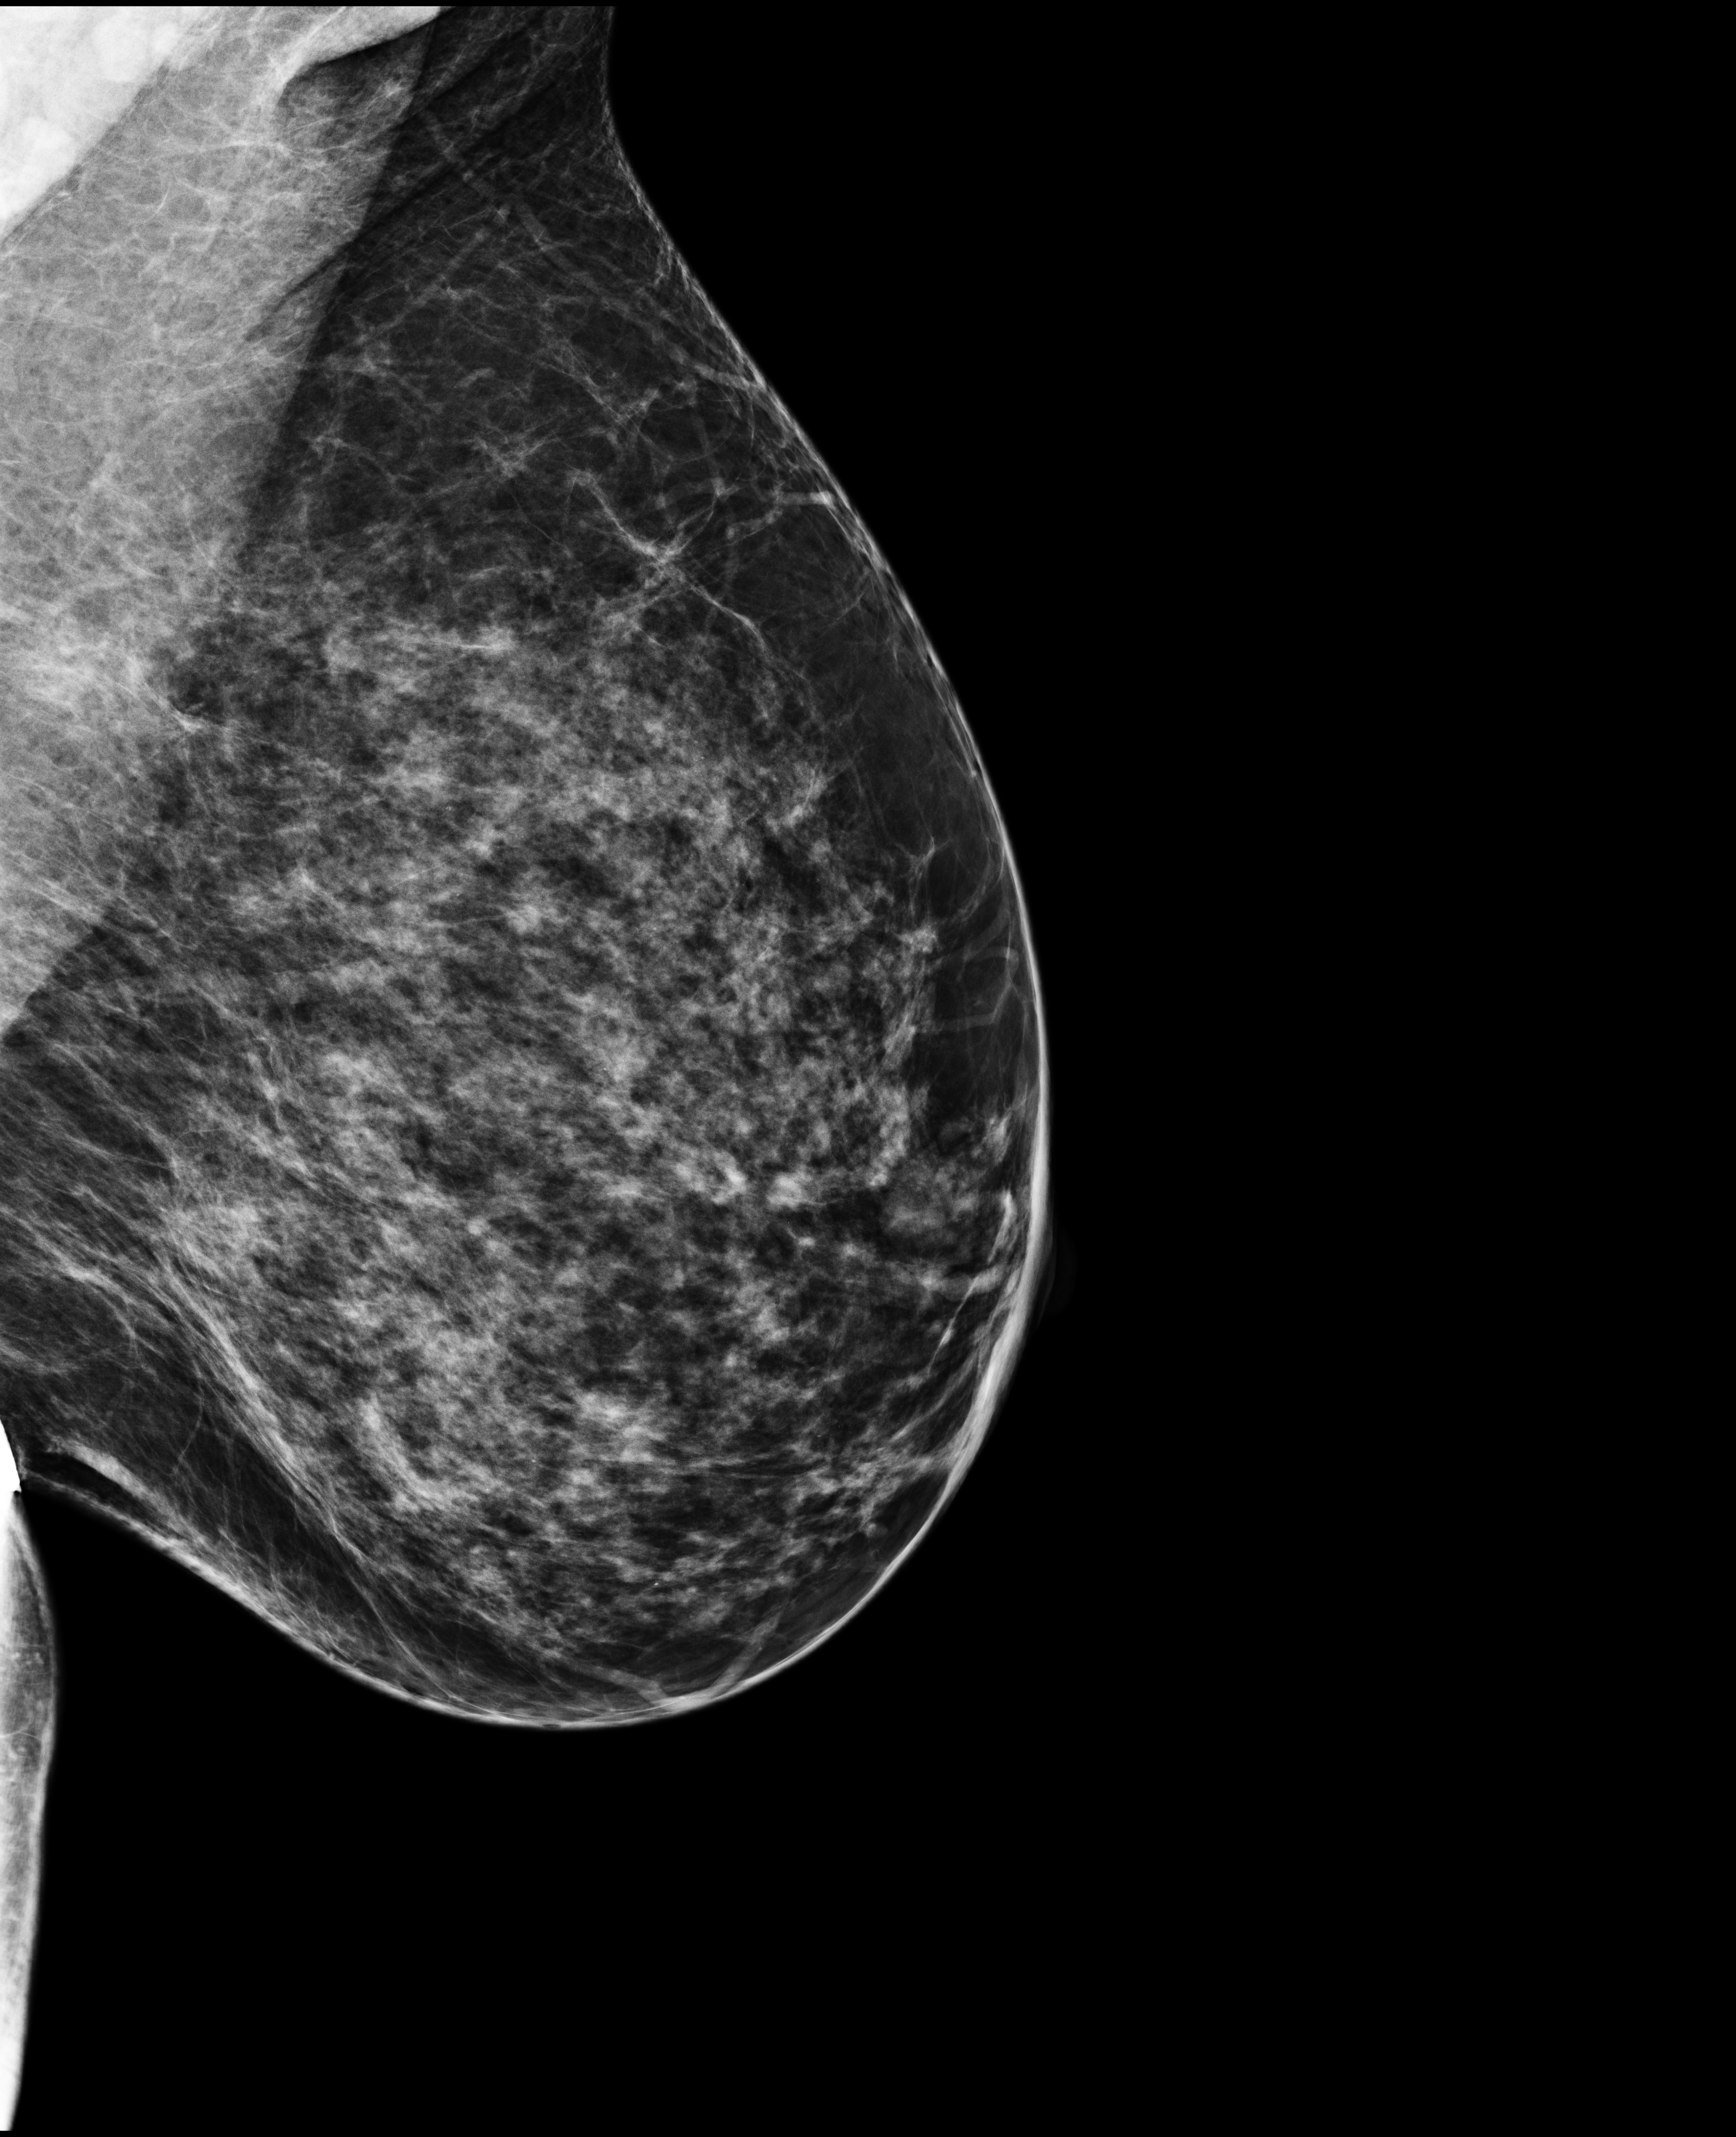
Digital mammogram (FFDM); left breast; medio-lateral oblique projection; screening examination; compressed breast thickness 80 mm. Patient: female, 50 years.
- BI-RADS breast density category at the screening exam (both breasts, scale 1–4): 3
- final BI-RADS assessment for this screening round (tomosynthesis exam, both breasts): category 1
- recall: no recall after this screen